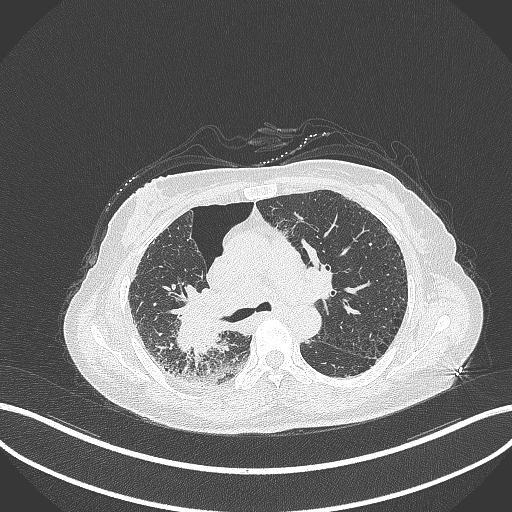
Chest CT, one axial slice. Slice 219 of 408 in the series (ordered by position). 120 kVp. Lung window (W 1500 / L -600 HU). 512 × 512 image matrix, field of view 400 × 400 mm. Patient: female, 64 years. From the clinical record (not read from this slice): clinical TNM (as recorded): T3 N3 M0.
Annotated regions visible in this slice (rectangle marked by the reading radiologist):
- lung tumour (recorded histology: squamous cell carcinoma): bounding box [x1, y1, x2, y2] px = [170, 284, 232, 358]